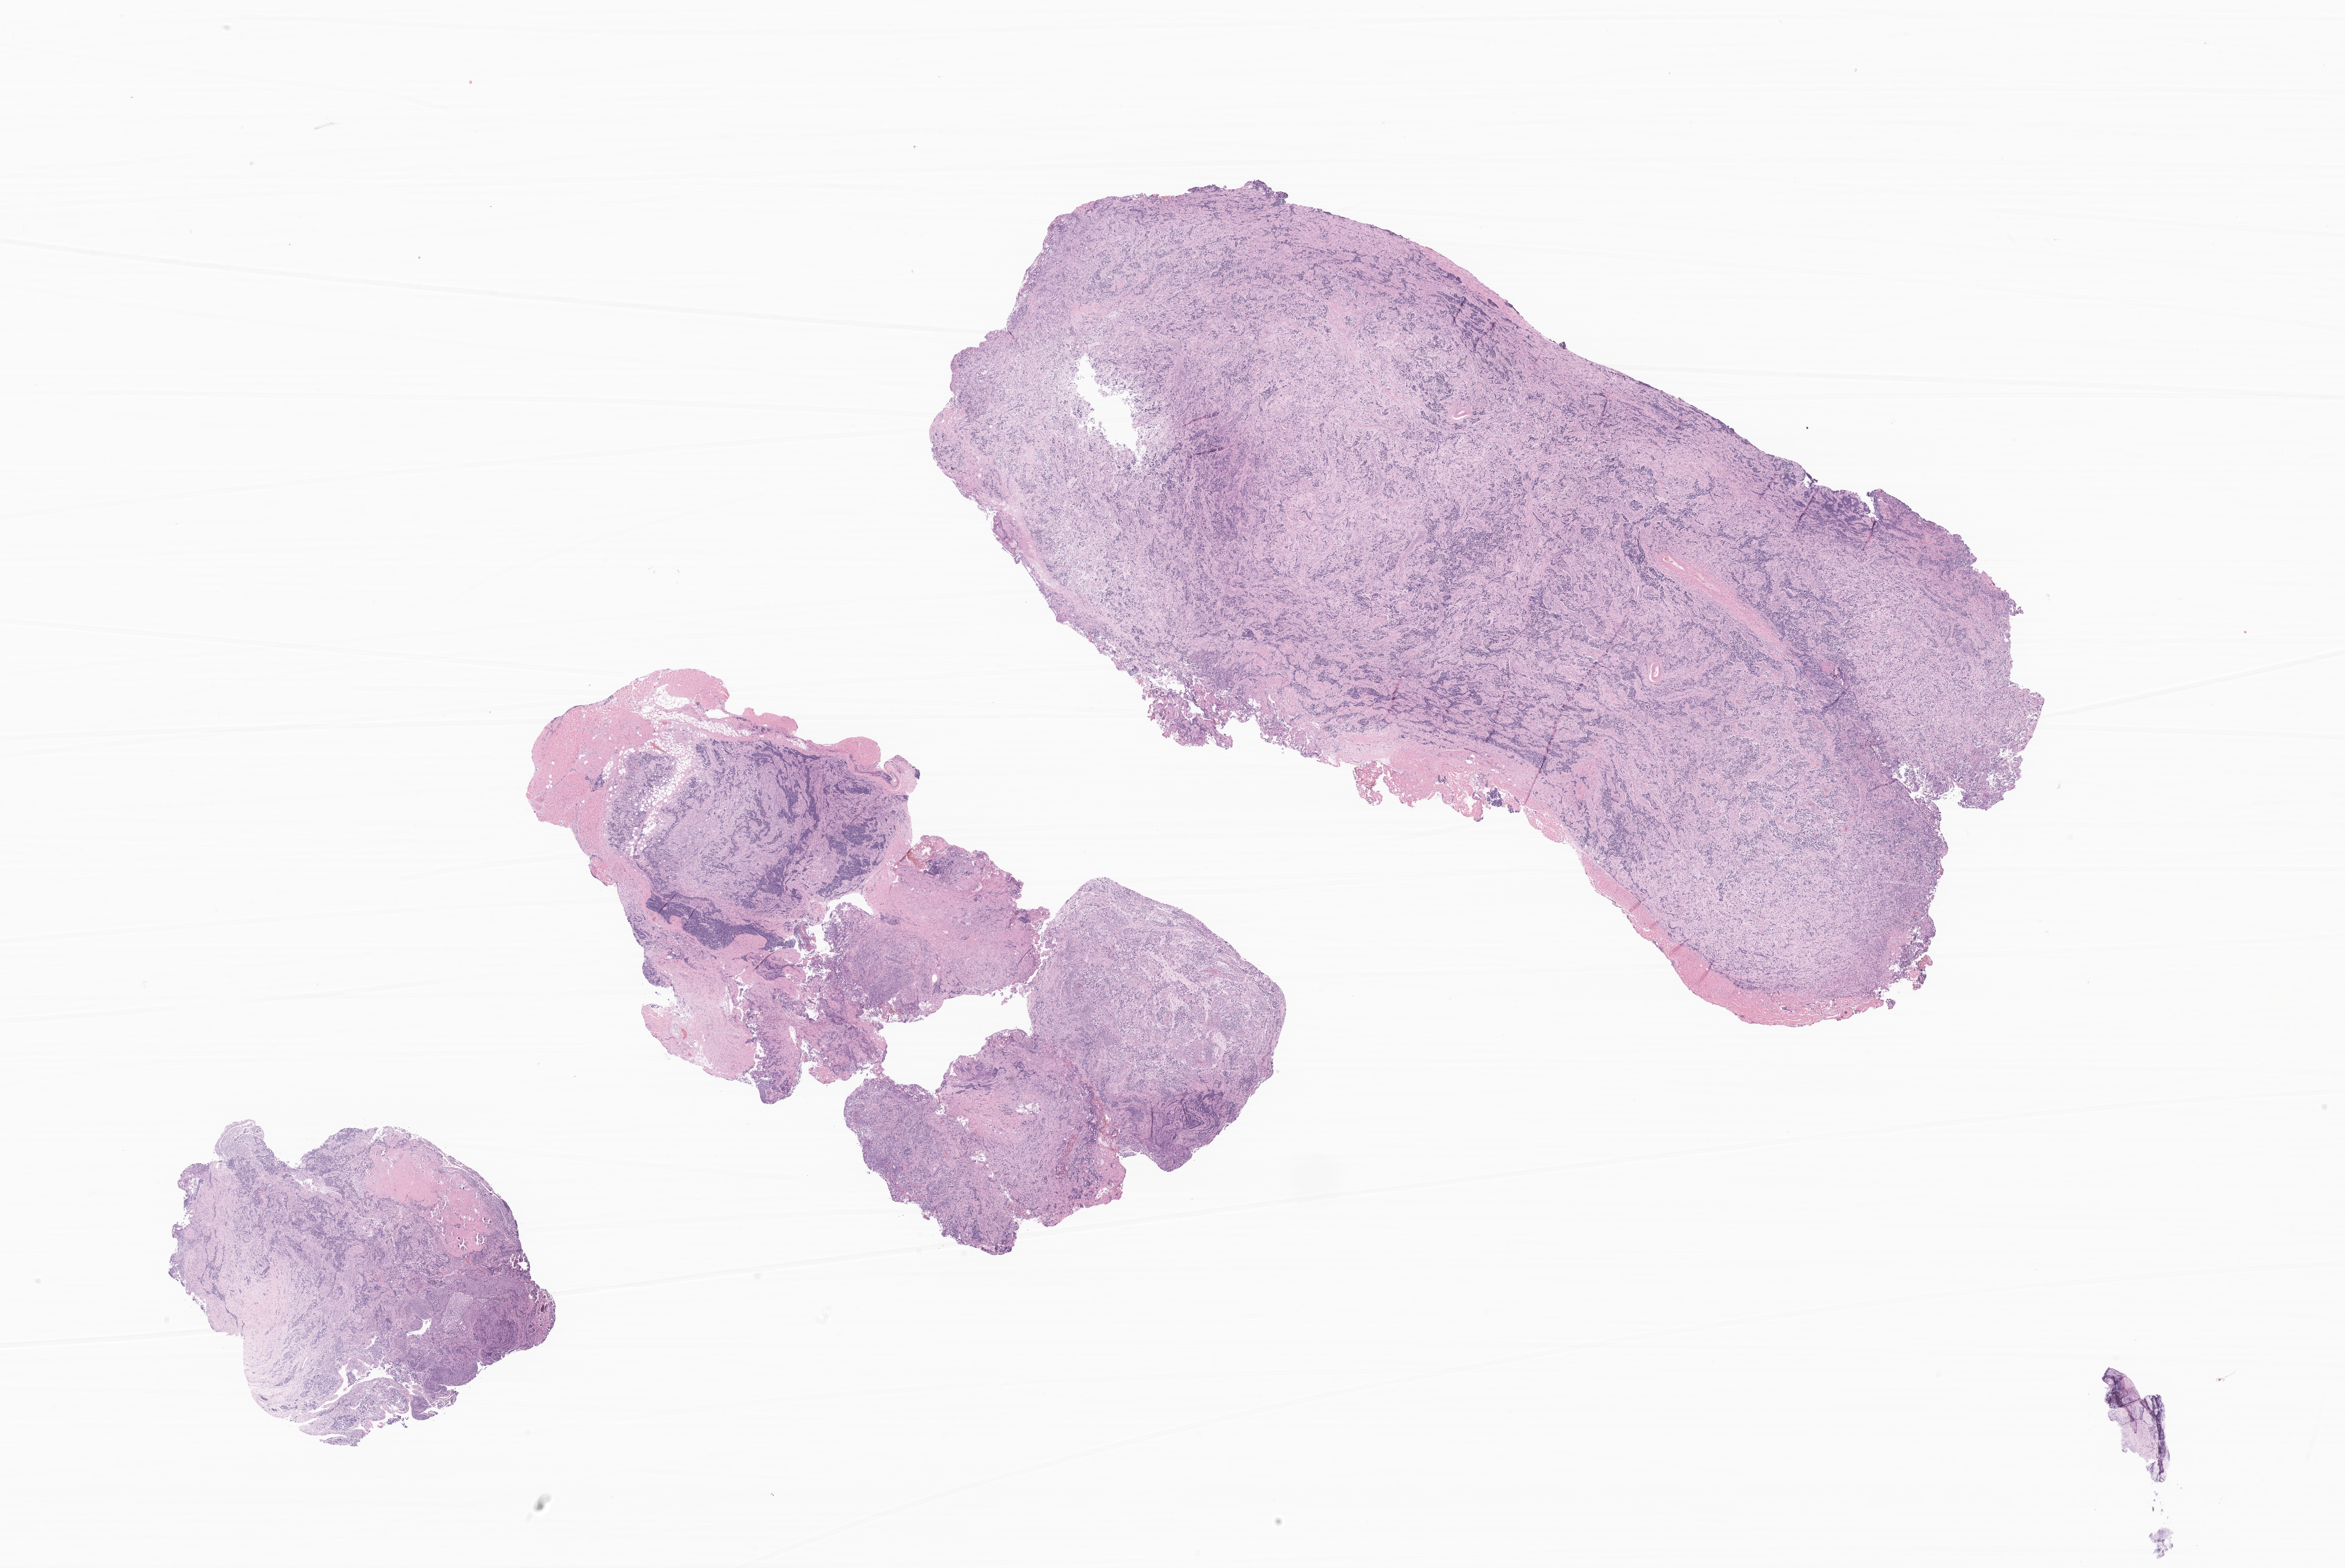
Digitized H&E-stained section of tumor tissue from the retroperitoneum — shown as a low-resolution overview of the whole scanned area (about 26.2 x 17.5 mm). Formalin-fixed, paraffin-embedded (FFPE) tissue. Patient male; age 220 days.
Recorded diagnosis: Neuroblastoma, NOS.